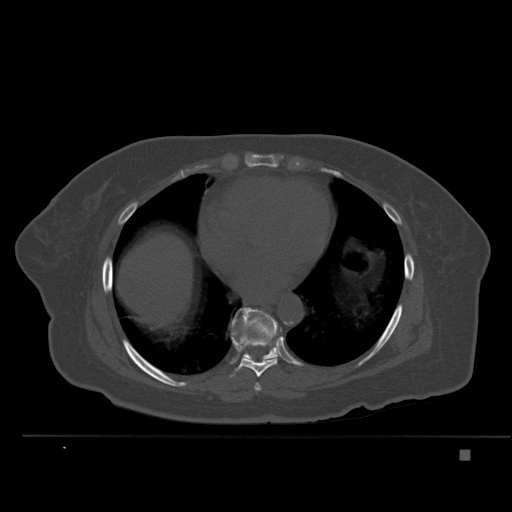
CT including the spine, one axial slice. Position 308 of 477 along the scan axis. Bone window (W 1800 / L 400 HU). 1.5 mm slice thickness. 512 × 512 image matrix. Female patient, age 74 years. From the clinical record (not read from this slice): primary cancer: colon.
Annotated regions visible in this slice (semi-automatic segmentation, software-assisted and operator-edited):
- T7 vertebra: bounding box [x1, y1, x2, y2] px = [254, 339, 268, 391]
- T8 vertebra: [231, 327, 279, 377]
- T9 vertebra: [232, 307, 279, 362]